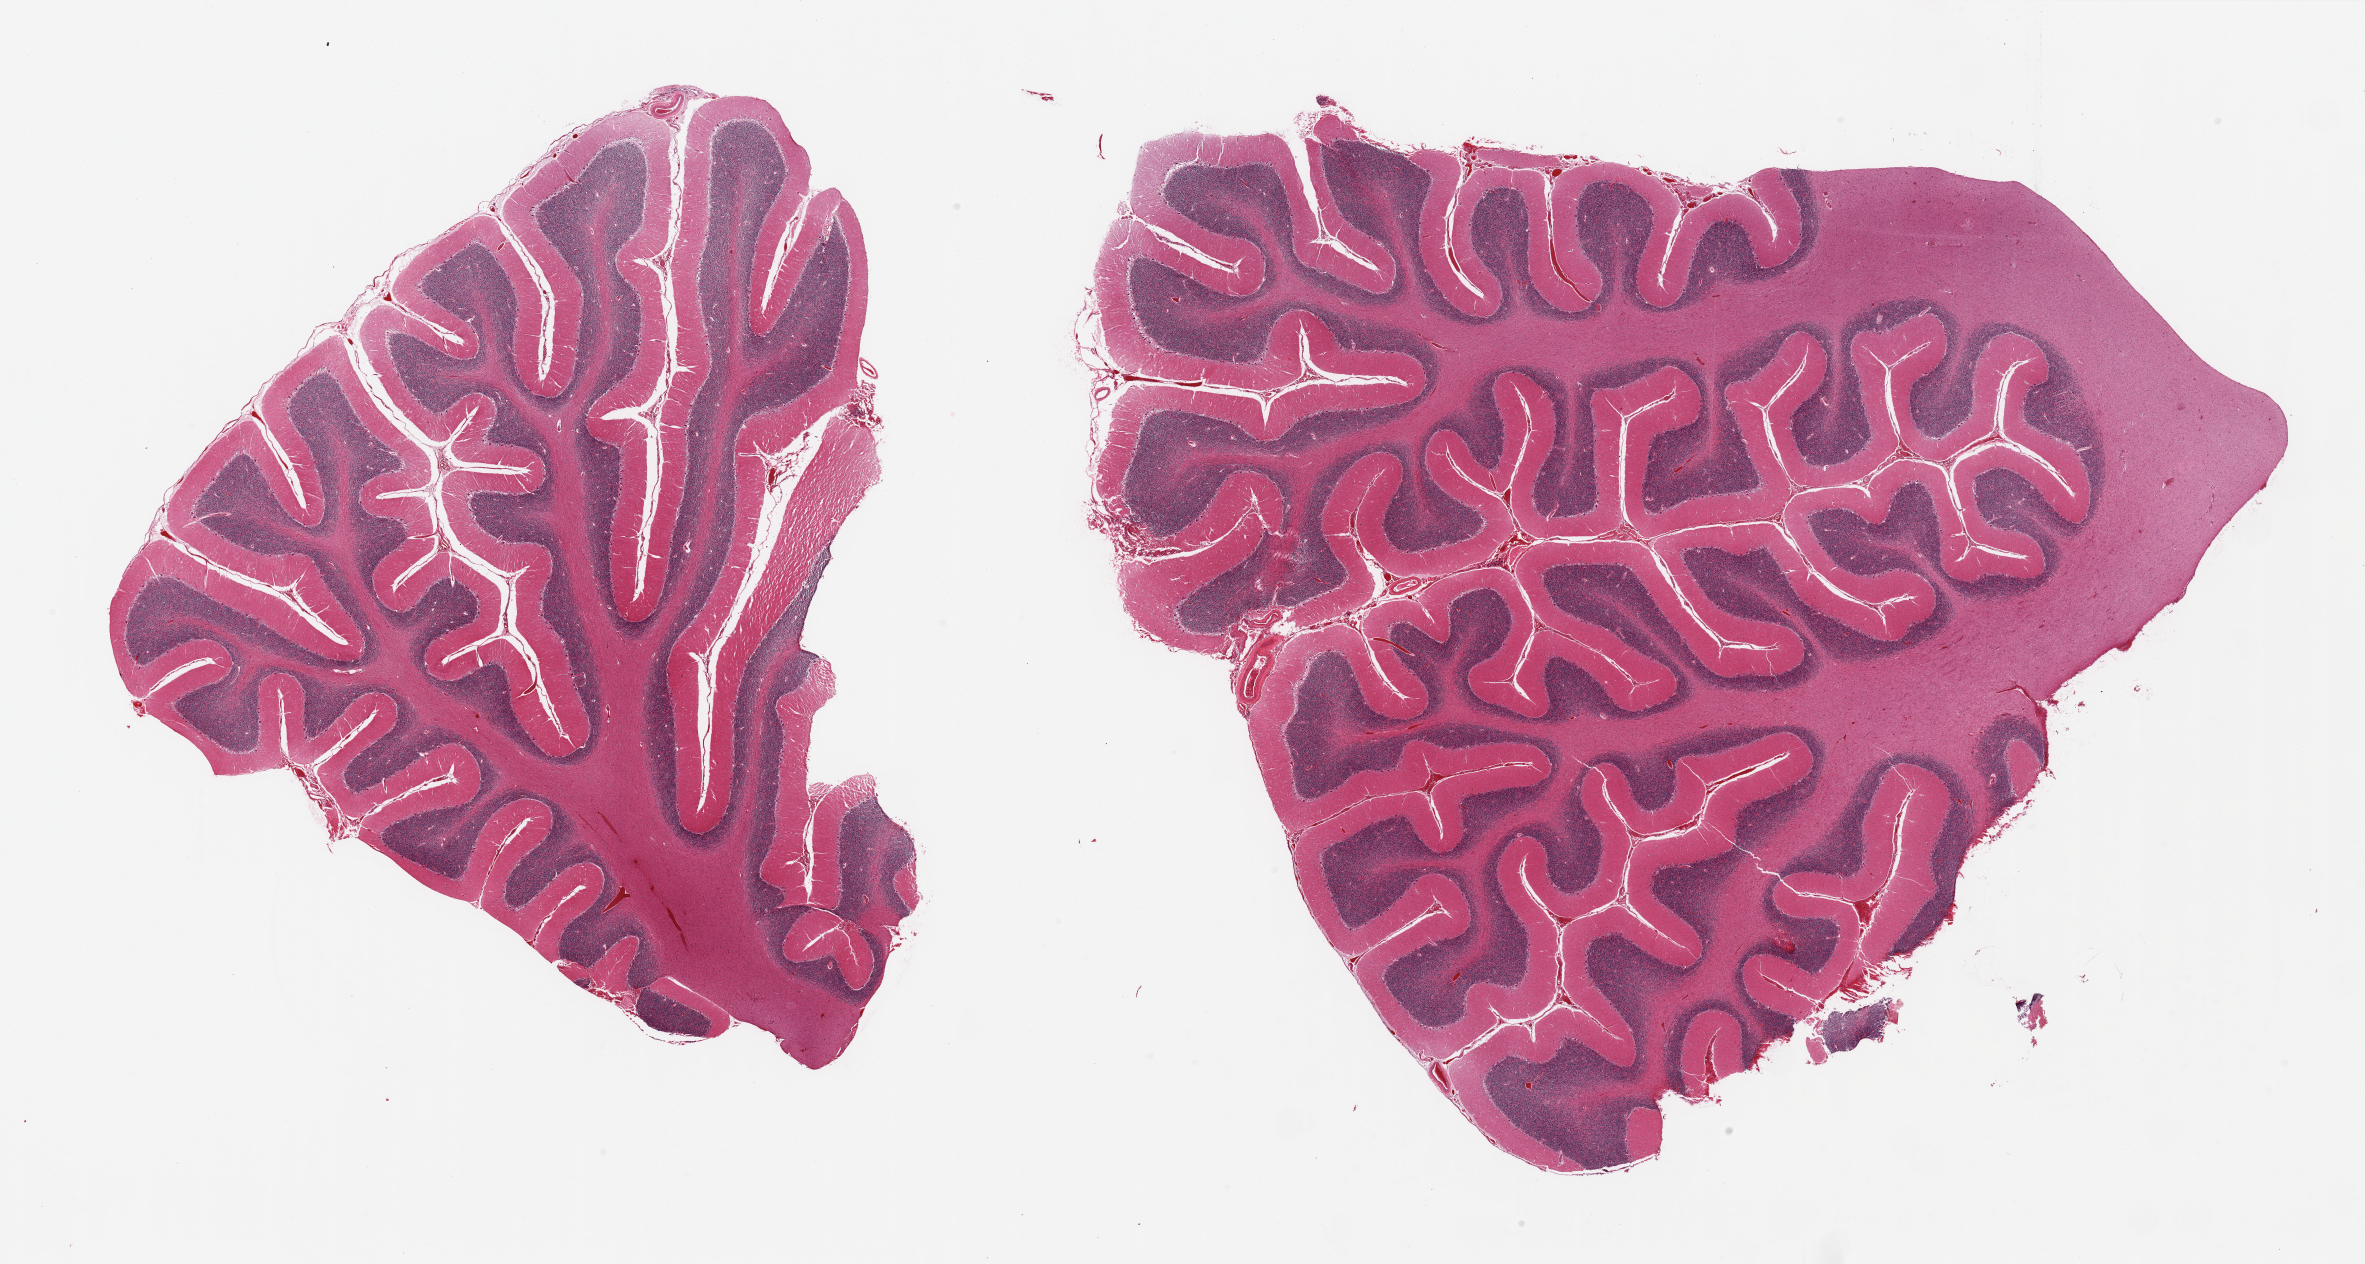
Digitized H&E-stained section — a low-resolution overview of the entire scanned area, about 37.4 x 20.0 mm; PAXgene-fixed paraffin-embedded (PFPE) section; sampled site (target tissue): cerebellum; tissue donor sample.
Pathologist's review note for this sample: 2 pieces.